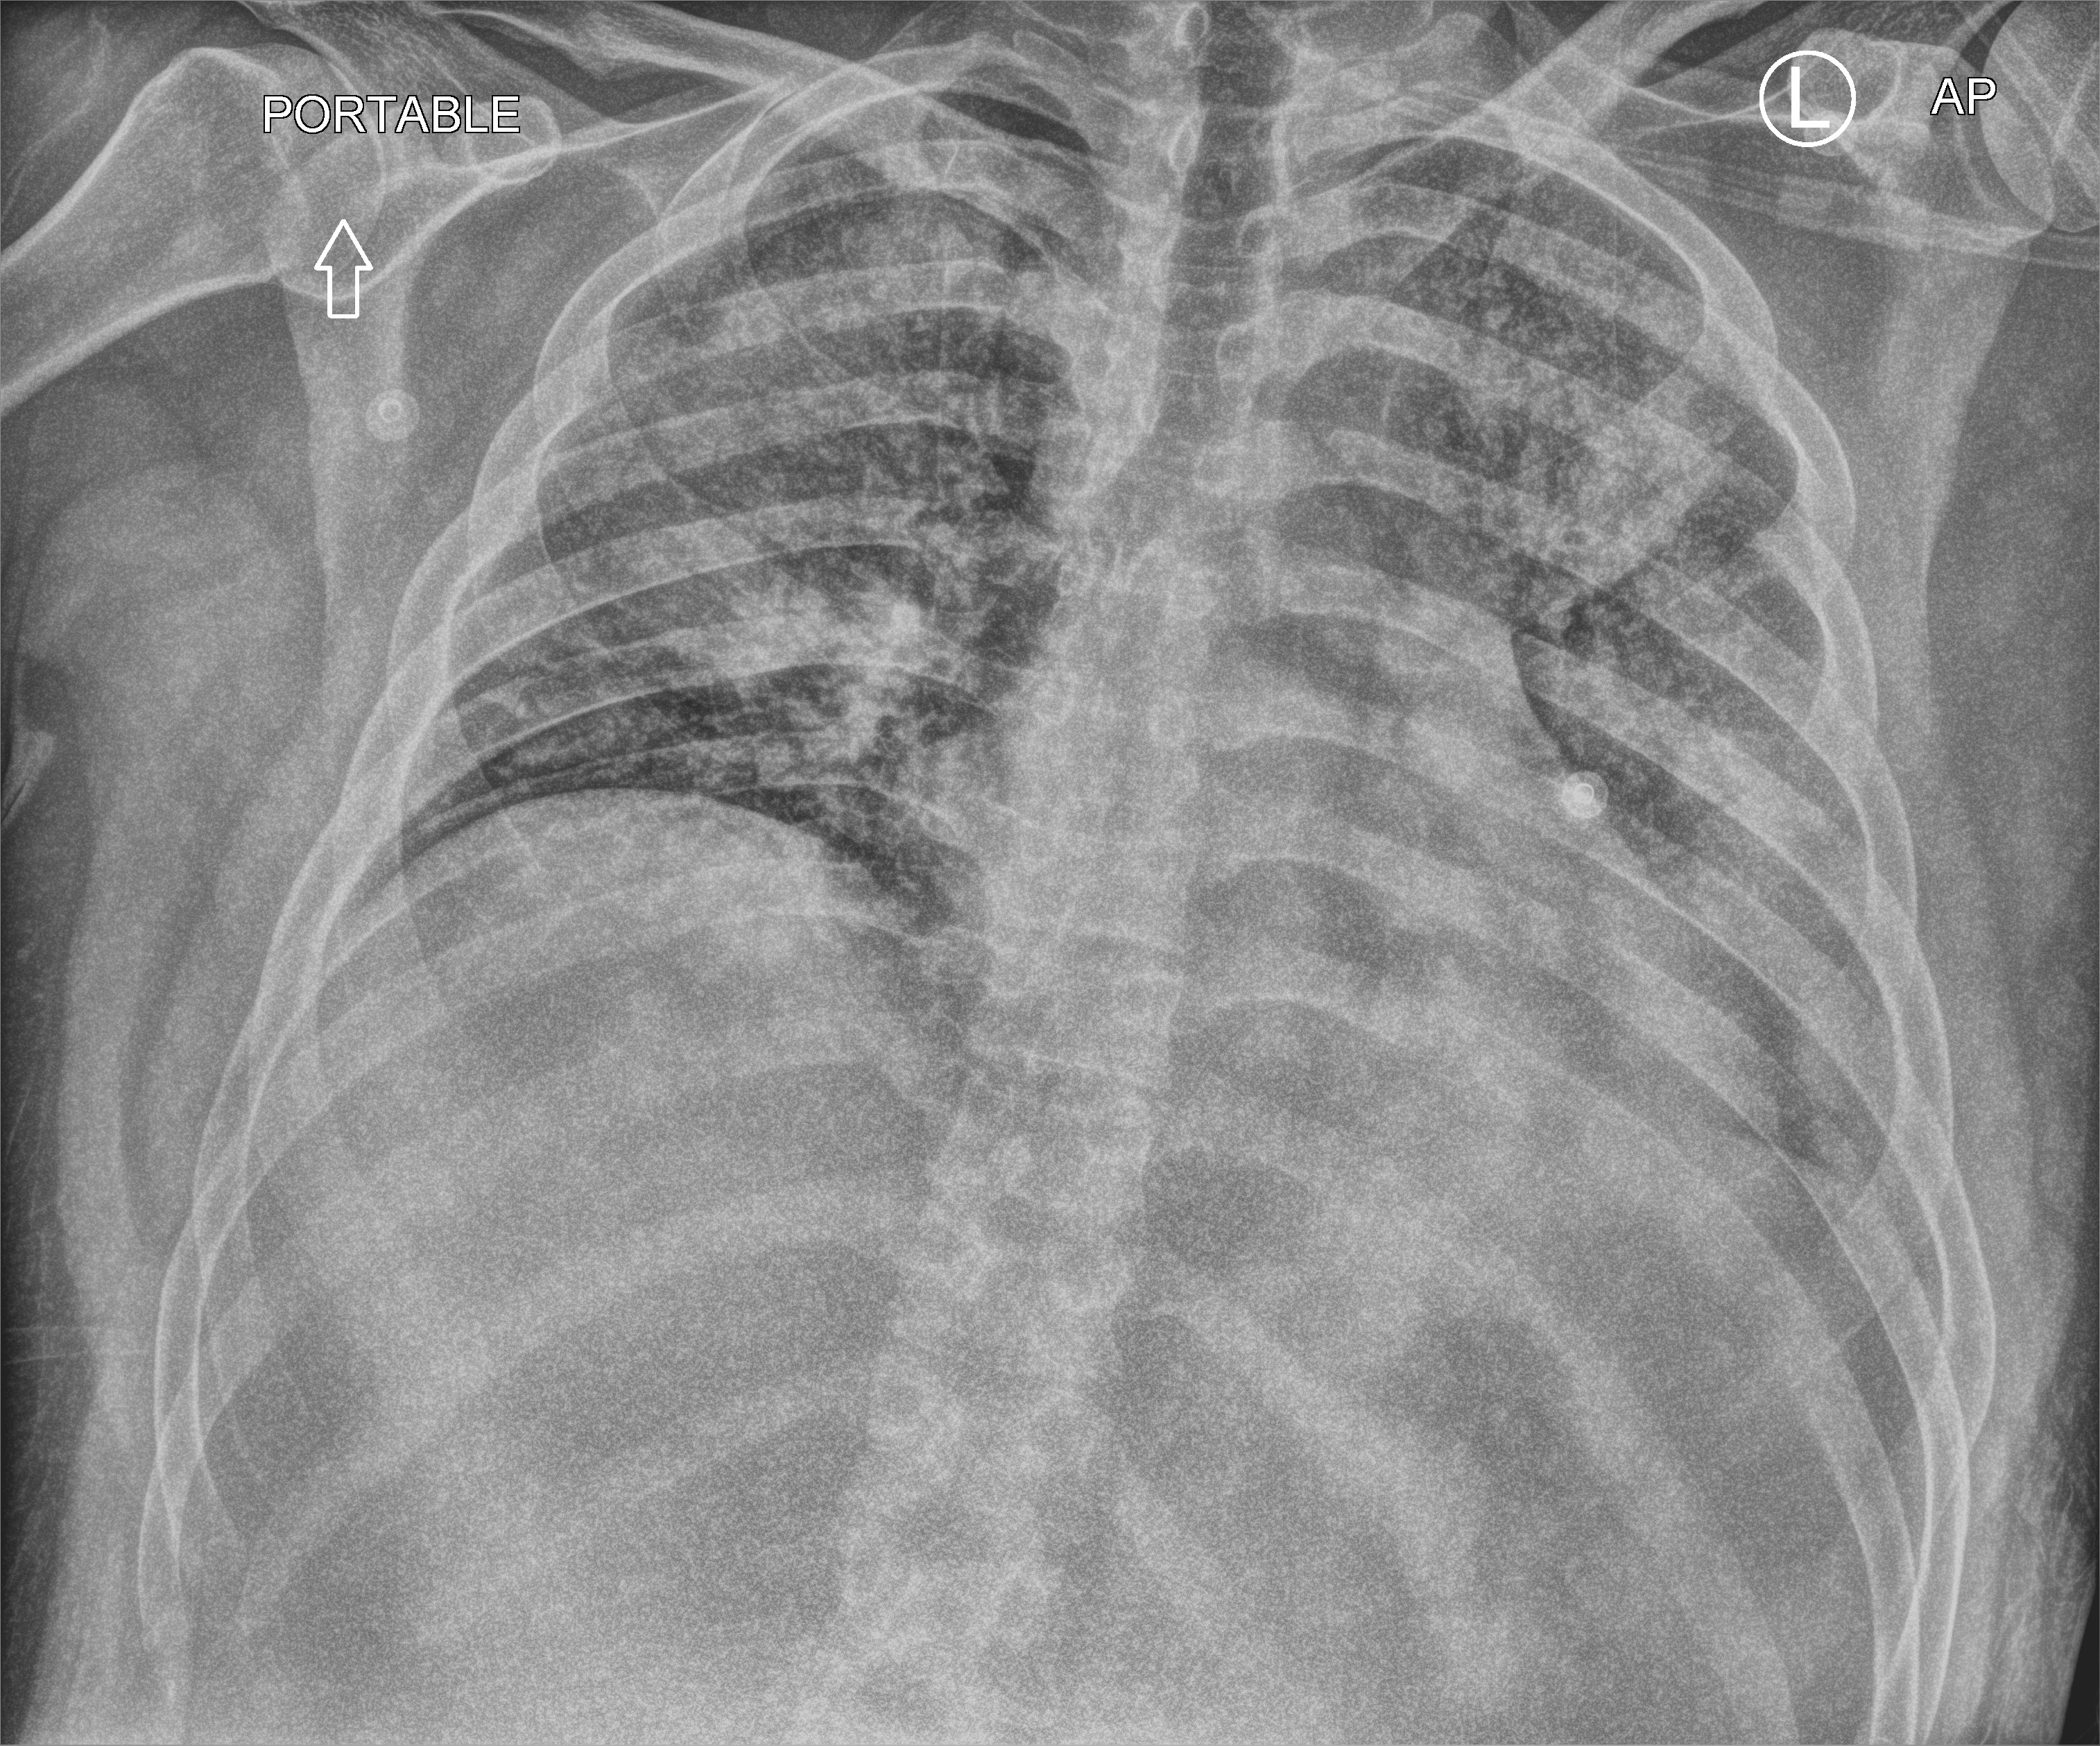
Bedside chest radiograph (computed radiography), anteroposterior (AP) projection. Male patient hospitalised with COVID-19, age 18–59 years.
Admission-level facts for this patient (not findings on this image; timing relative to this image not recorded):
- hypertension (admission record): yes
- smoking status (admission record): current
- length of hospital stay: 61 days